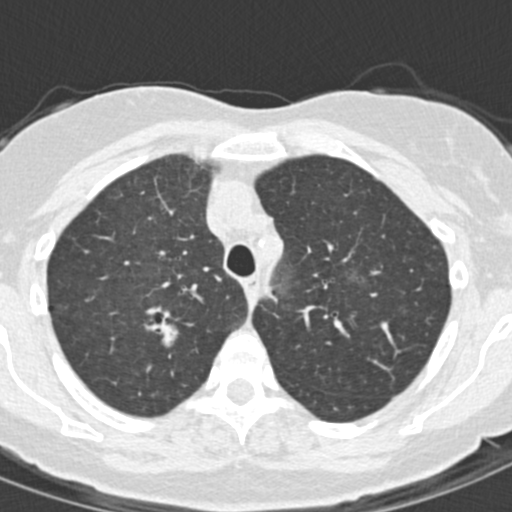
Low-dose screening chest CT, one axial slice. Slice 117 of 157 in the series (ordered by position). Reconstruction kernel B30f. 120 kVp. Lung window (W 1500 / L -600 HU). 2 mm slice thickness. 512 × 512 image matrix.
Structures marked on this image (outlined manually by an expert reader):
- lesion 1 (tumor, upper lobe of right lung): bounding box <143,316,180,354> (left, top, right, bottom; pixels)